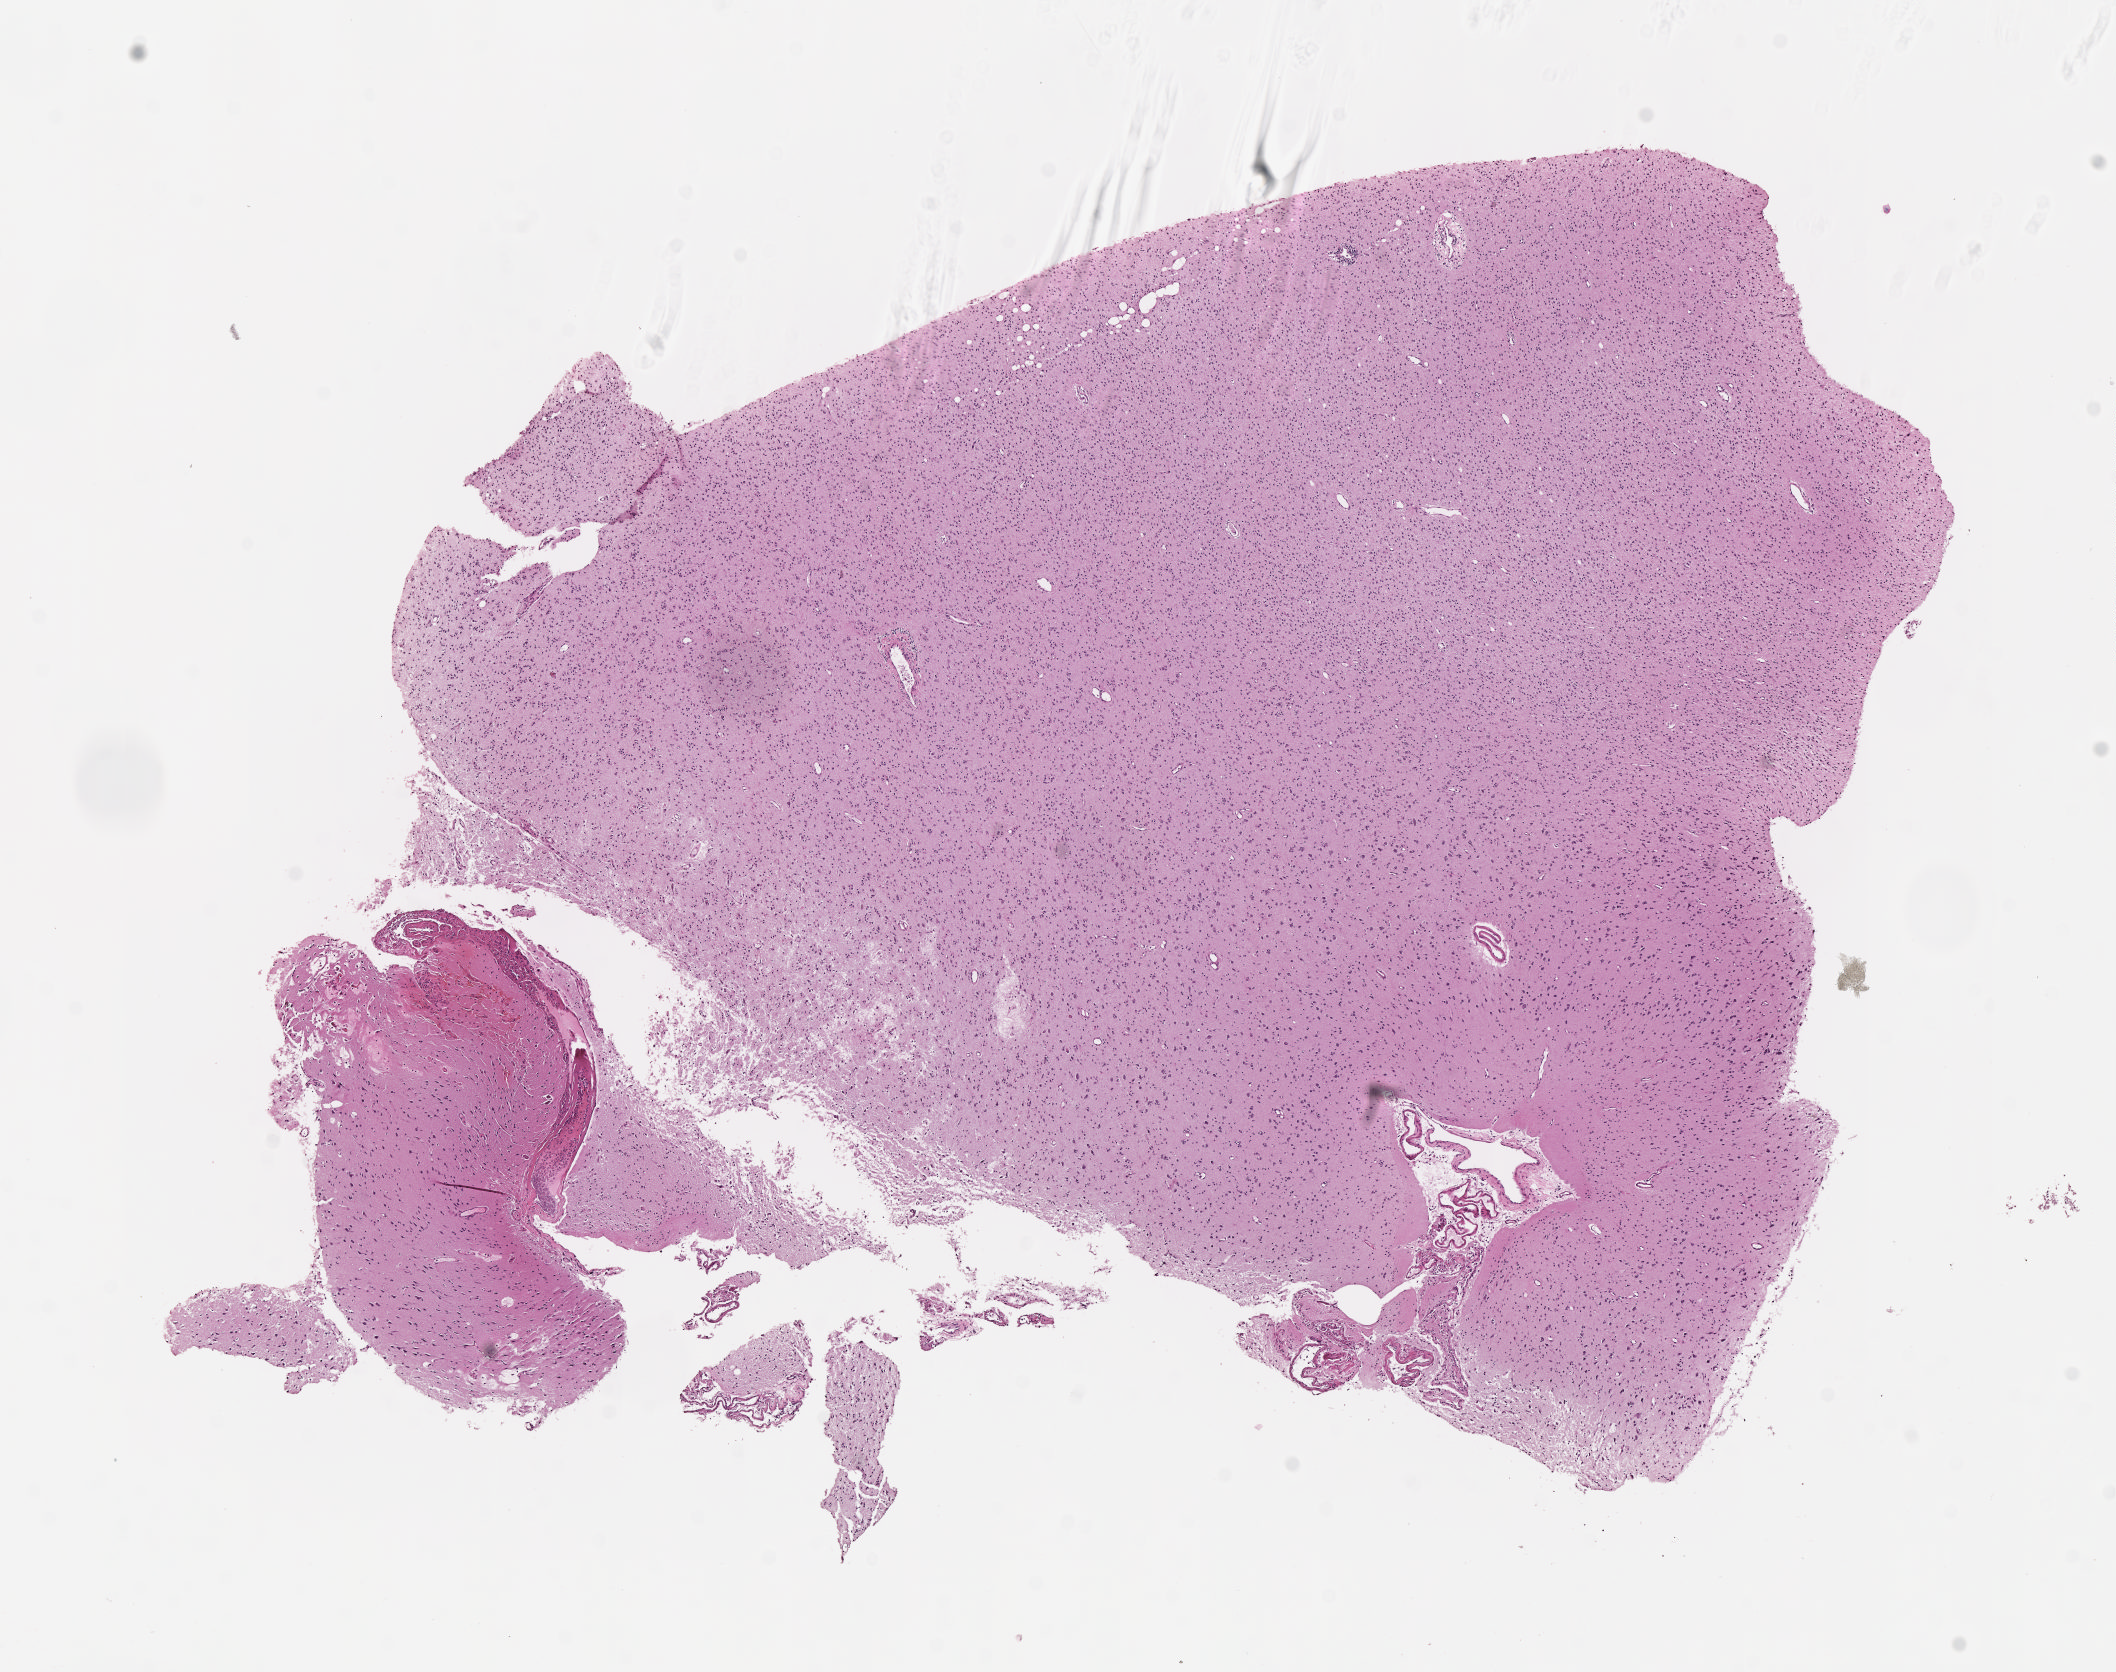
Whole-slide histology image, Hematoxylin and eosin (H&E) stained — a low-resolution overview of the entire scanned area, about 8.6 x 6.8 mm; FFPE section; brain, primary tumour sample. Male patient; age at initial diagnosis 40 years. Histologic grade: G2 (moderately differentiated).
Histologic diagnosis: Oligodendroglioma, NOS (cerebrum).